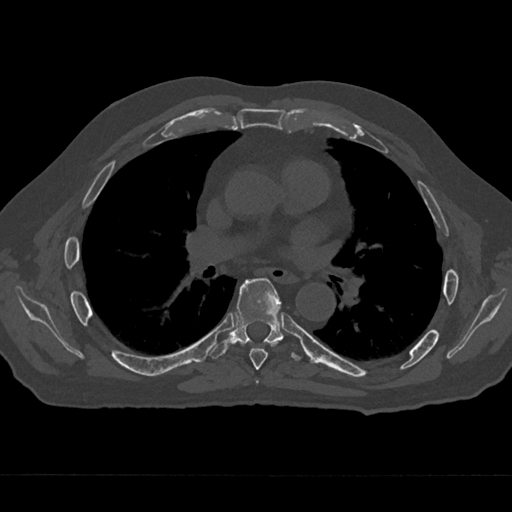
CT including the spine, one axial slice. Position 395 of 797 along the scan axis. Reconstruction kernel Br40s/3. 120 kVp. Bone window (W 1800 / L 400 HU). 0.5 mm slice thickness. 512 × 512 image matrix. Patient: male, 75 years. Case-level facts recorded for this patient, not image findings: primary cancer: renal.
Annotated regions visible in this slice (semi-automatically segmented with operator editing):
- T5 vertebra: bounding box <257,380,259,383> (left, top, right, bottom; pixels)
- T6 vertebra: <240,342,278,370>
- T7 vertebra: <209,278,303,360>